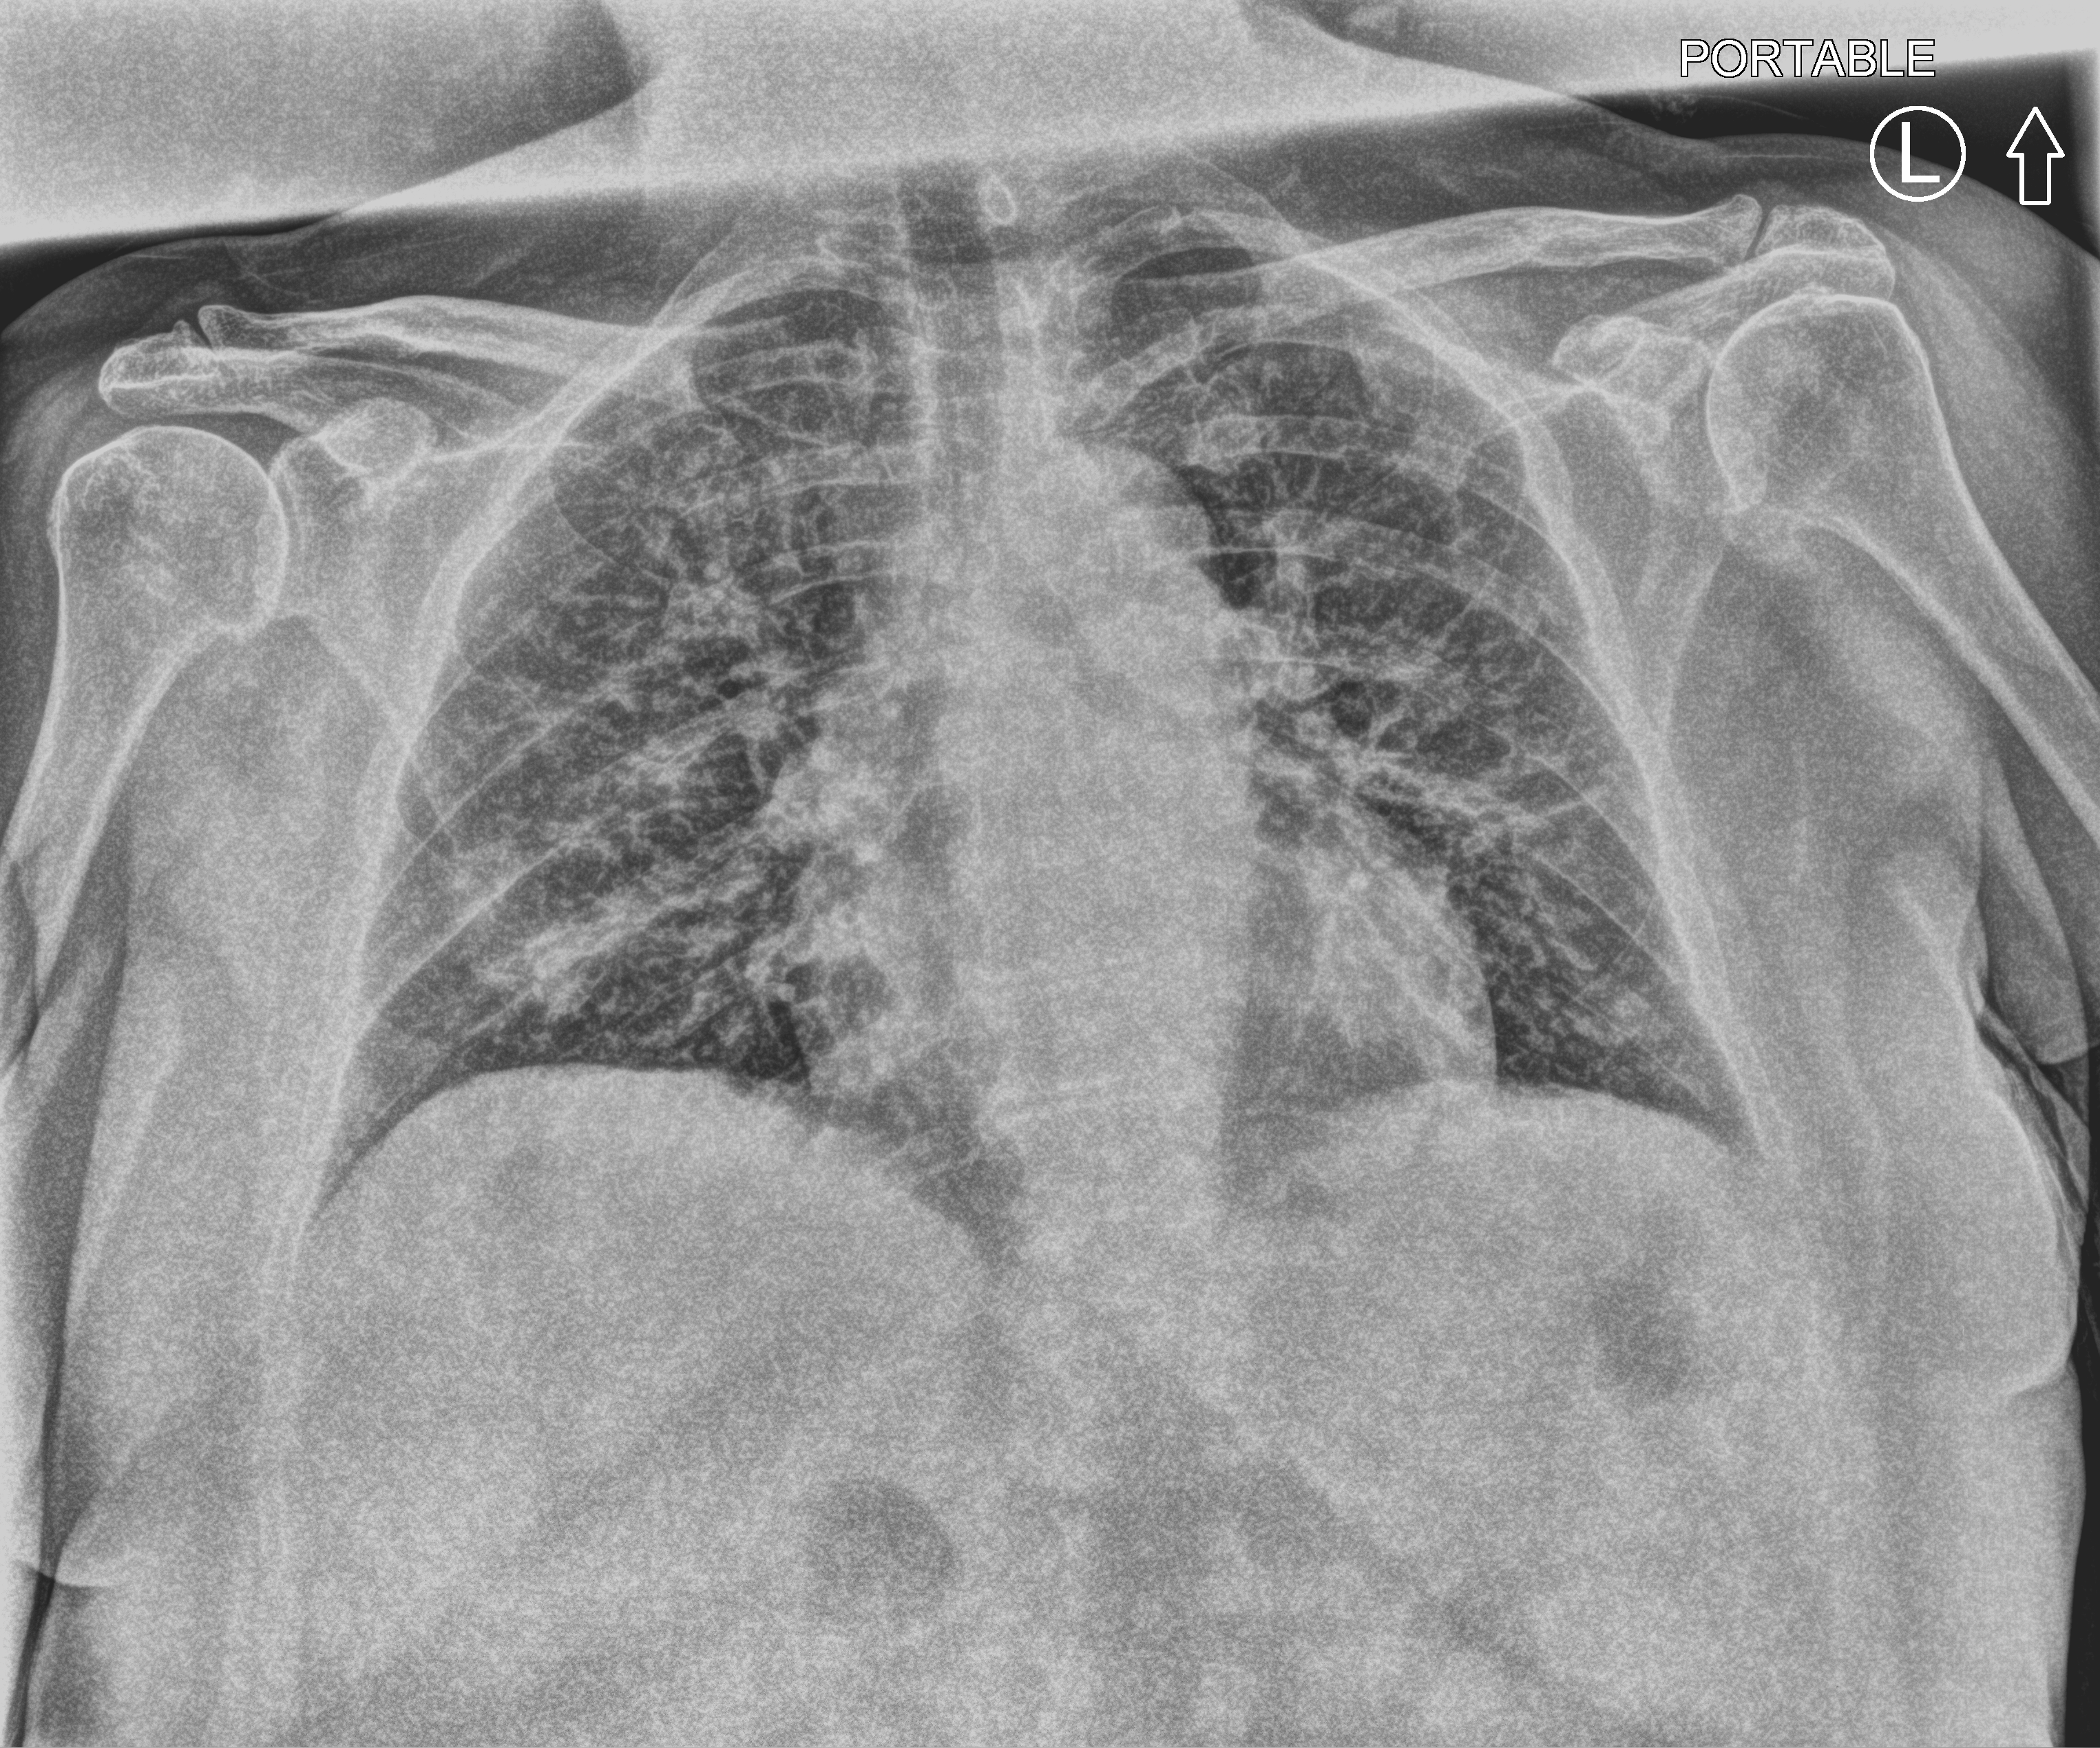
Chest radiograph, anteroposterior (AP) projection. Female patient hospitalised with COVID-19, age 60–74 years.
Hospital-stay facts (about this admission, not read from this image; timing relative to this image not recorded): mechanically ventilated during this hospital stay: no; COPD (admission record): no.